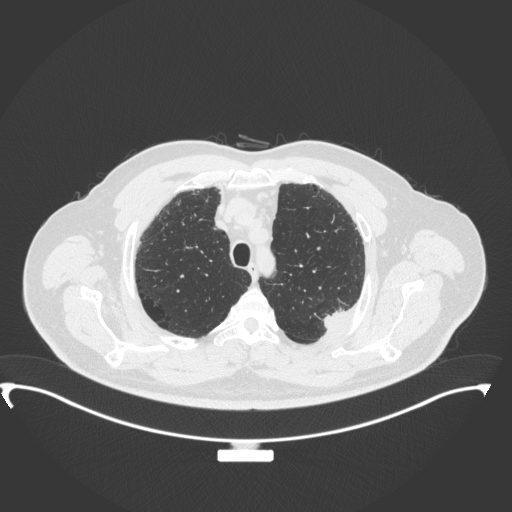
Chest CT, one axial slice. Position 291 of 350 along the scan axis. Lung window (W 1500 / L -600 HU). 1 mm slice thickness. 512 × 512 image matrix, field of view 459 × 459 mm. Patient: male, 64 years. From the clinical record (not read from this slice): clinical TNM (as recorded): T1c N1 M1.
Structures marked on this image (rectangle marked by the reading radiologist):
- lung tumour (recorded histology: adenocarcinoma): box from (x=312, y=301) to (x=350, y=333) px